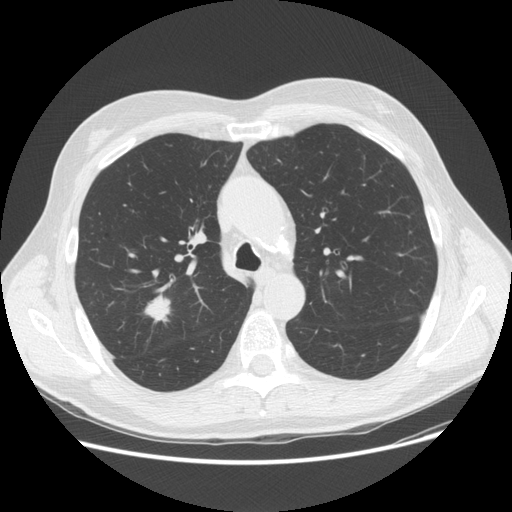
Low-dose screening chest CT, one axial slice. 120 kVp. Lung window (W 1500 / L -600 HU). 512 × 512 image matrix.
Annotated regions visible in this slice (manually delineated by an expert):
- lesion 1 (tumor, upper lobe of right lung): bounding box <144,292,171,323> (left, top, right, bottom; pixels)